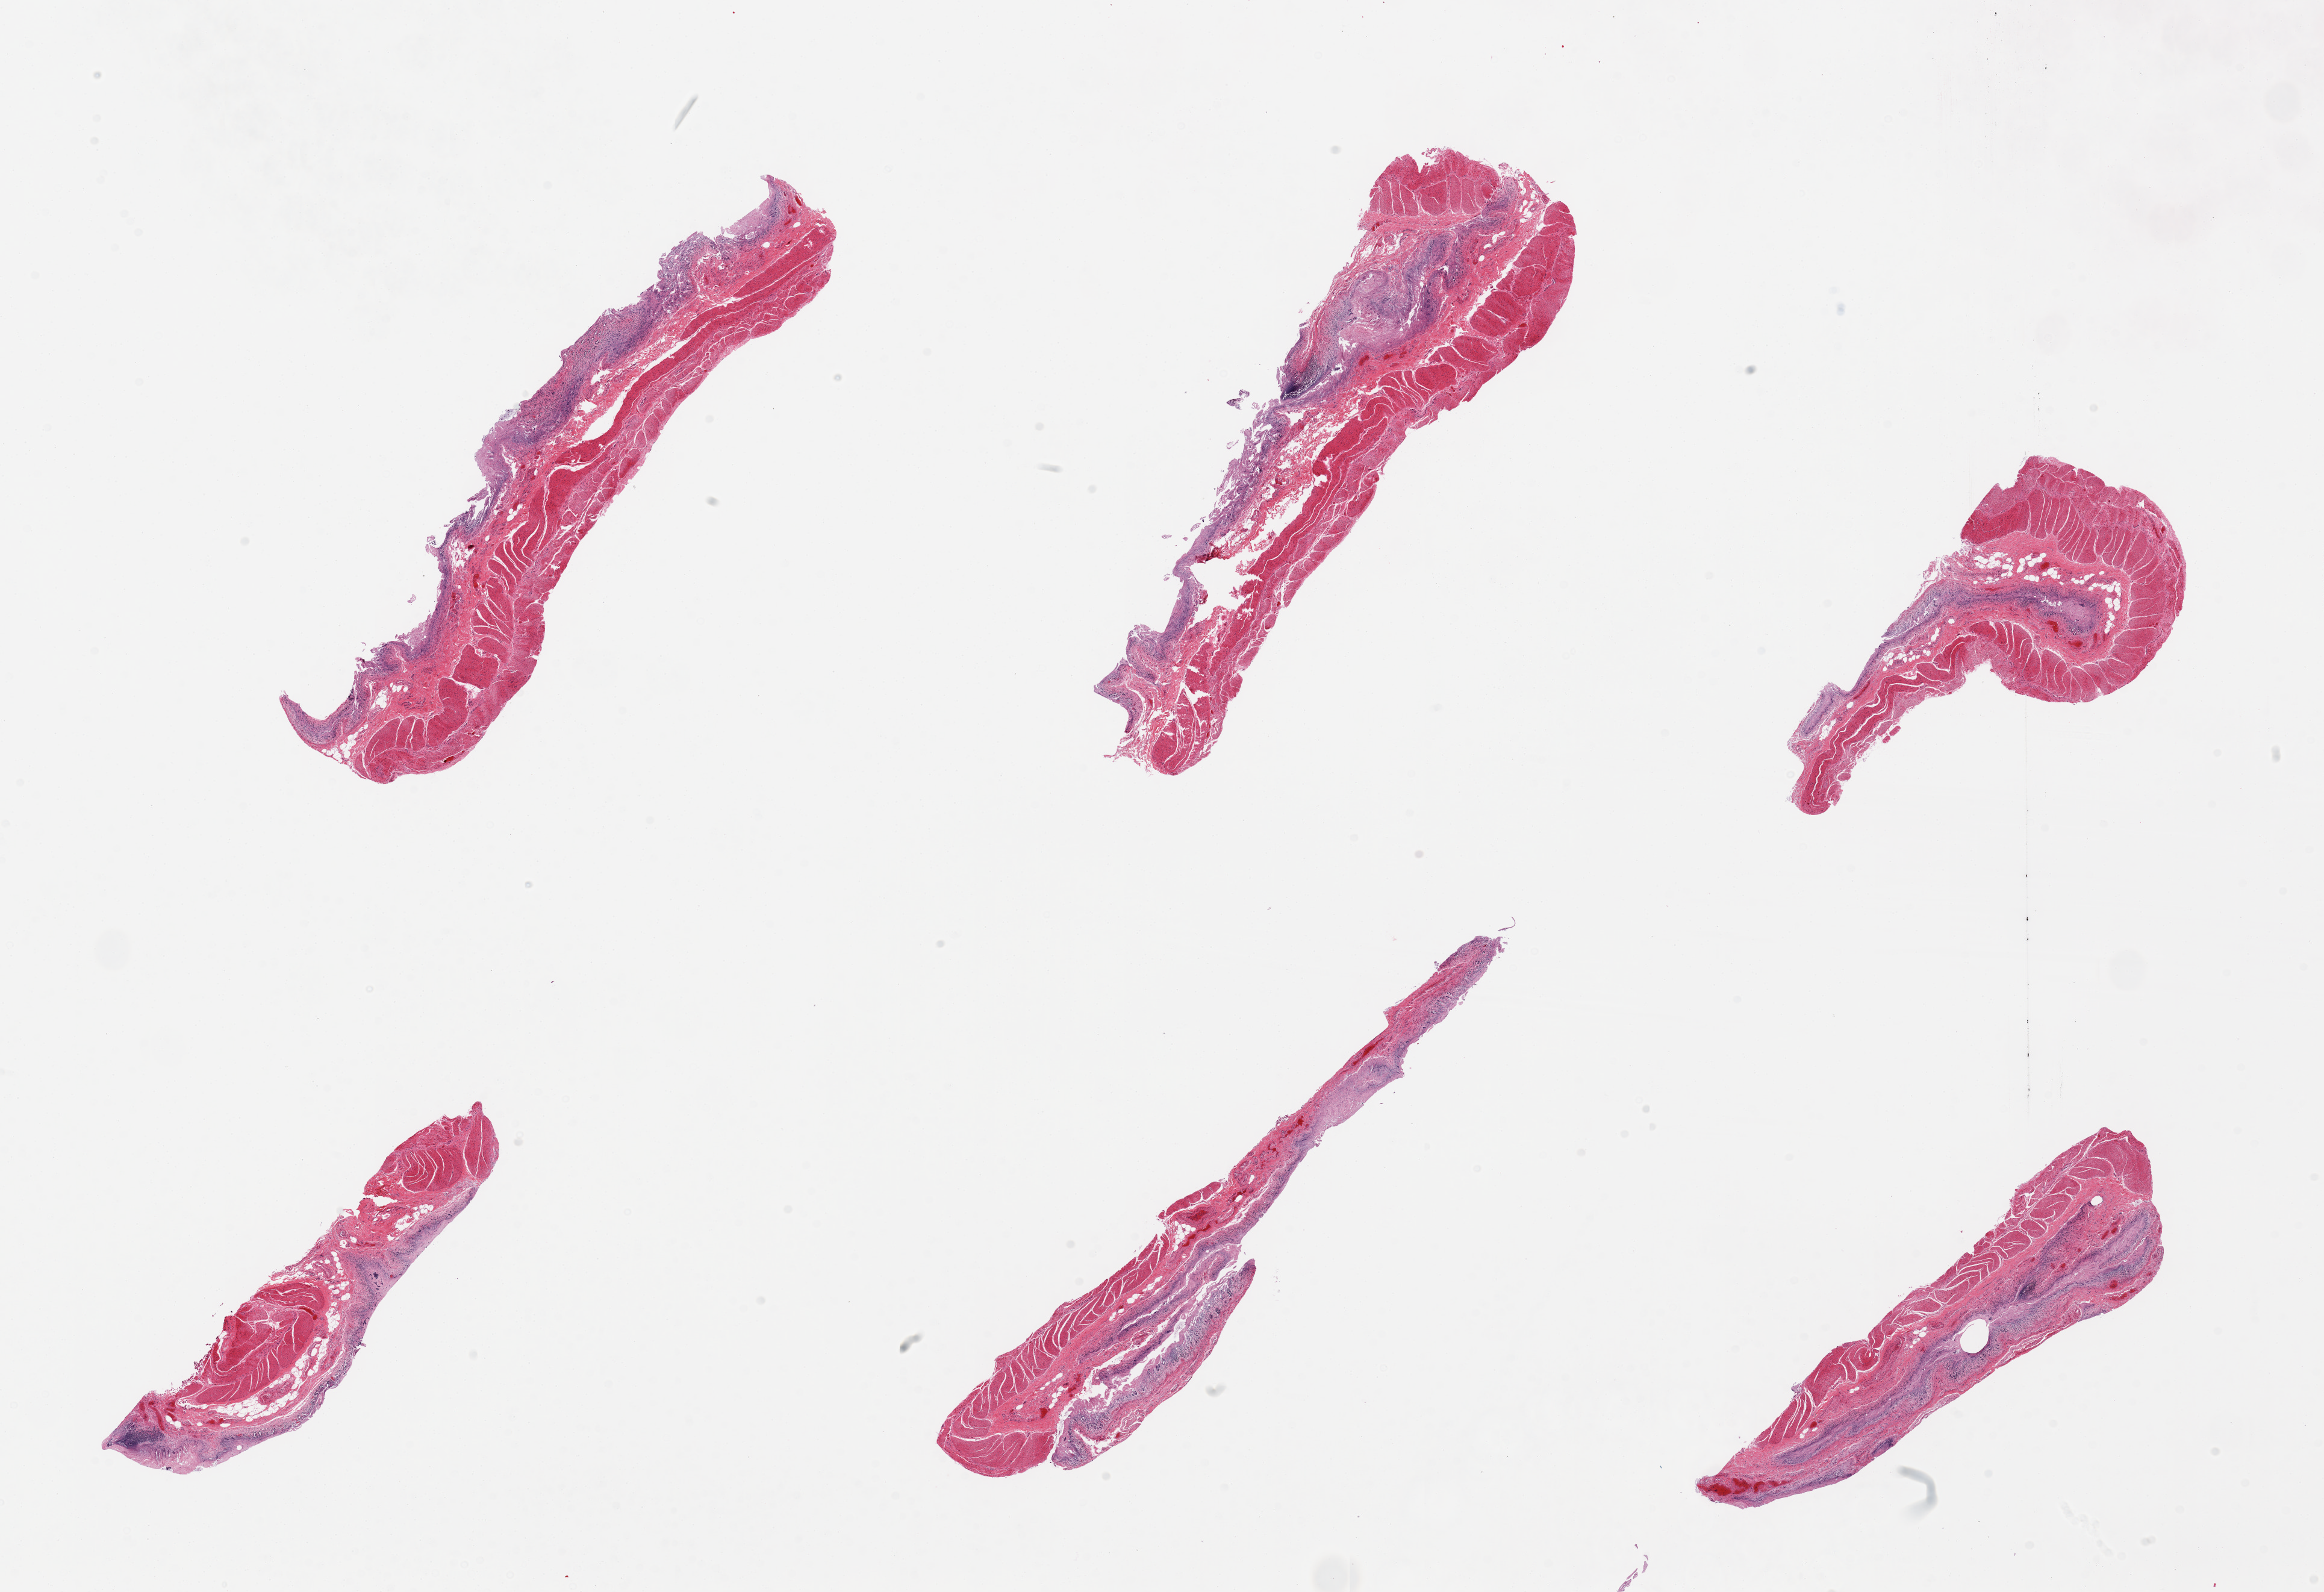
H&E whole-slide image, brightfield, a low-resolution overview of the entire scanned area, about 30.5 x 20.9 mm; PAXgene-fixed paraffin-embedded (PFPE) section; sampled site (target tissue): ileum; tissue donor sample. Donor: male.
Reviewer comment on this tissue sample: 6 pieces, severely autolyzed mucosa with only focal residual lymphoid cells, muscularis (not target).